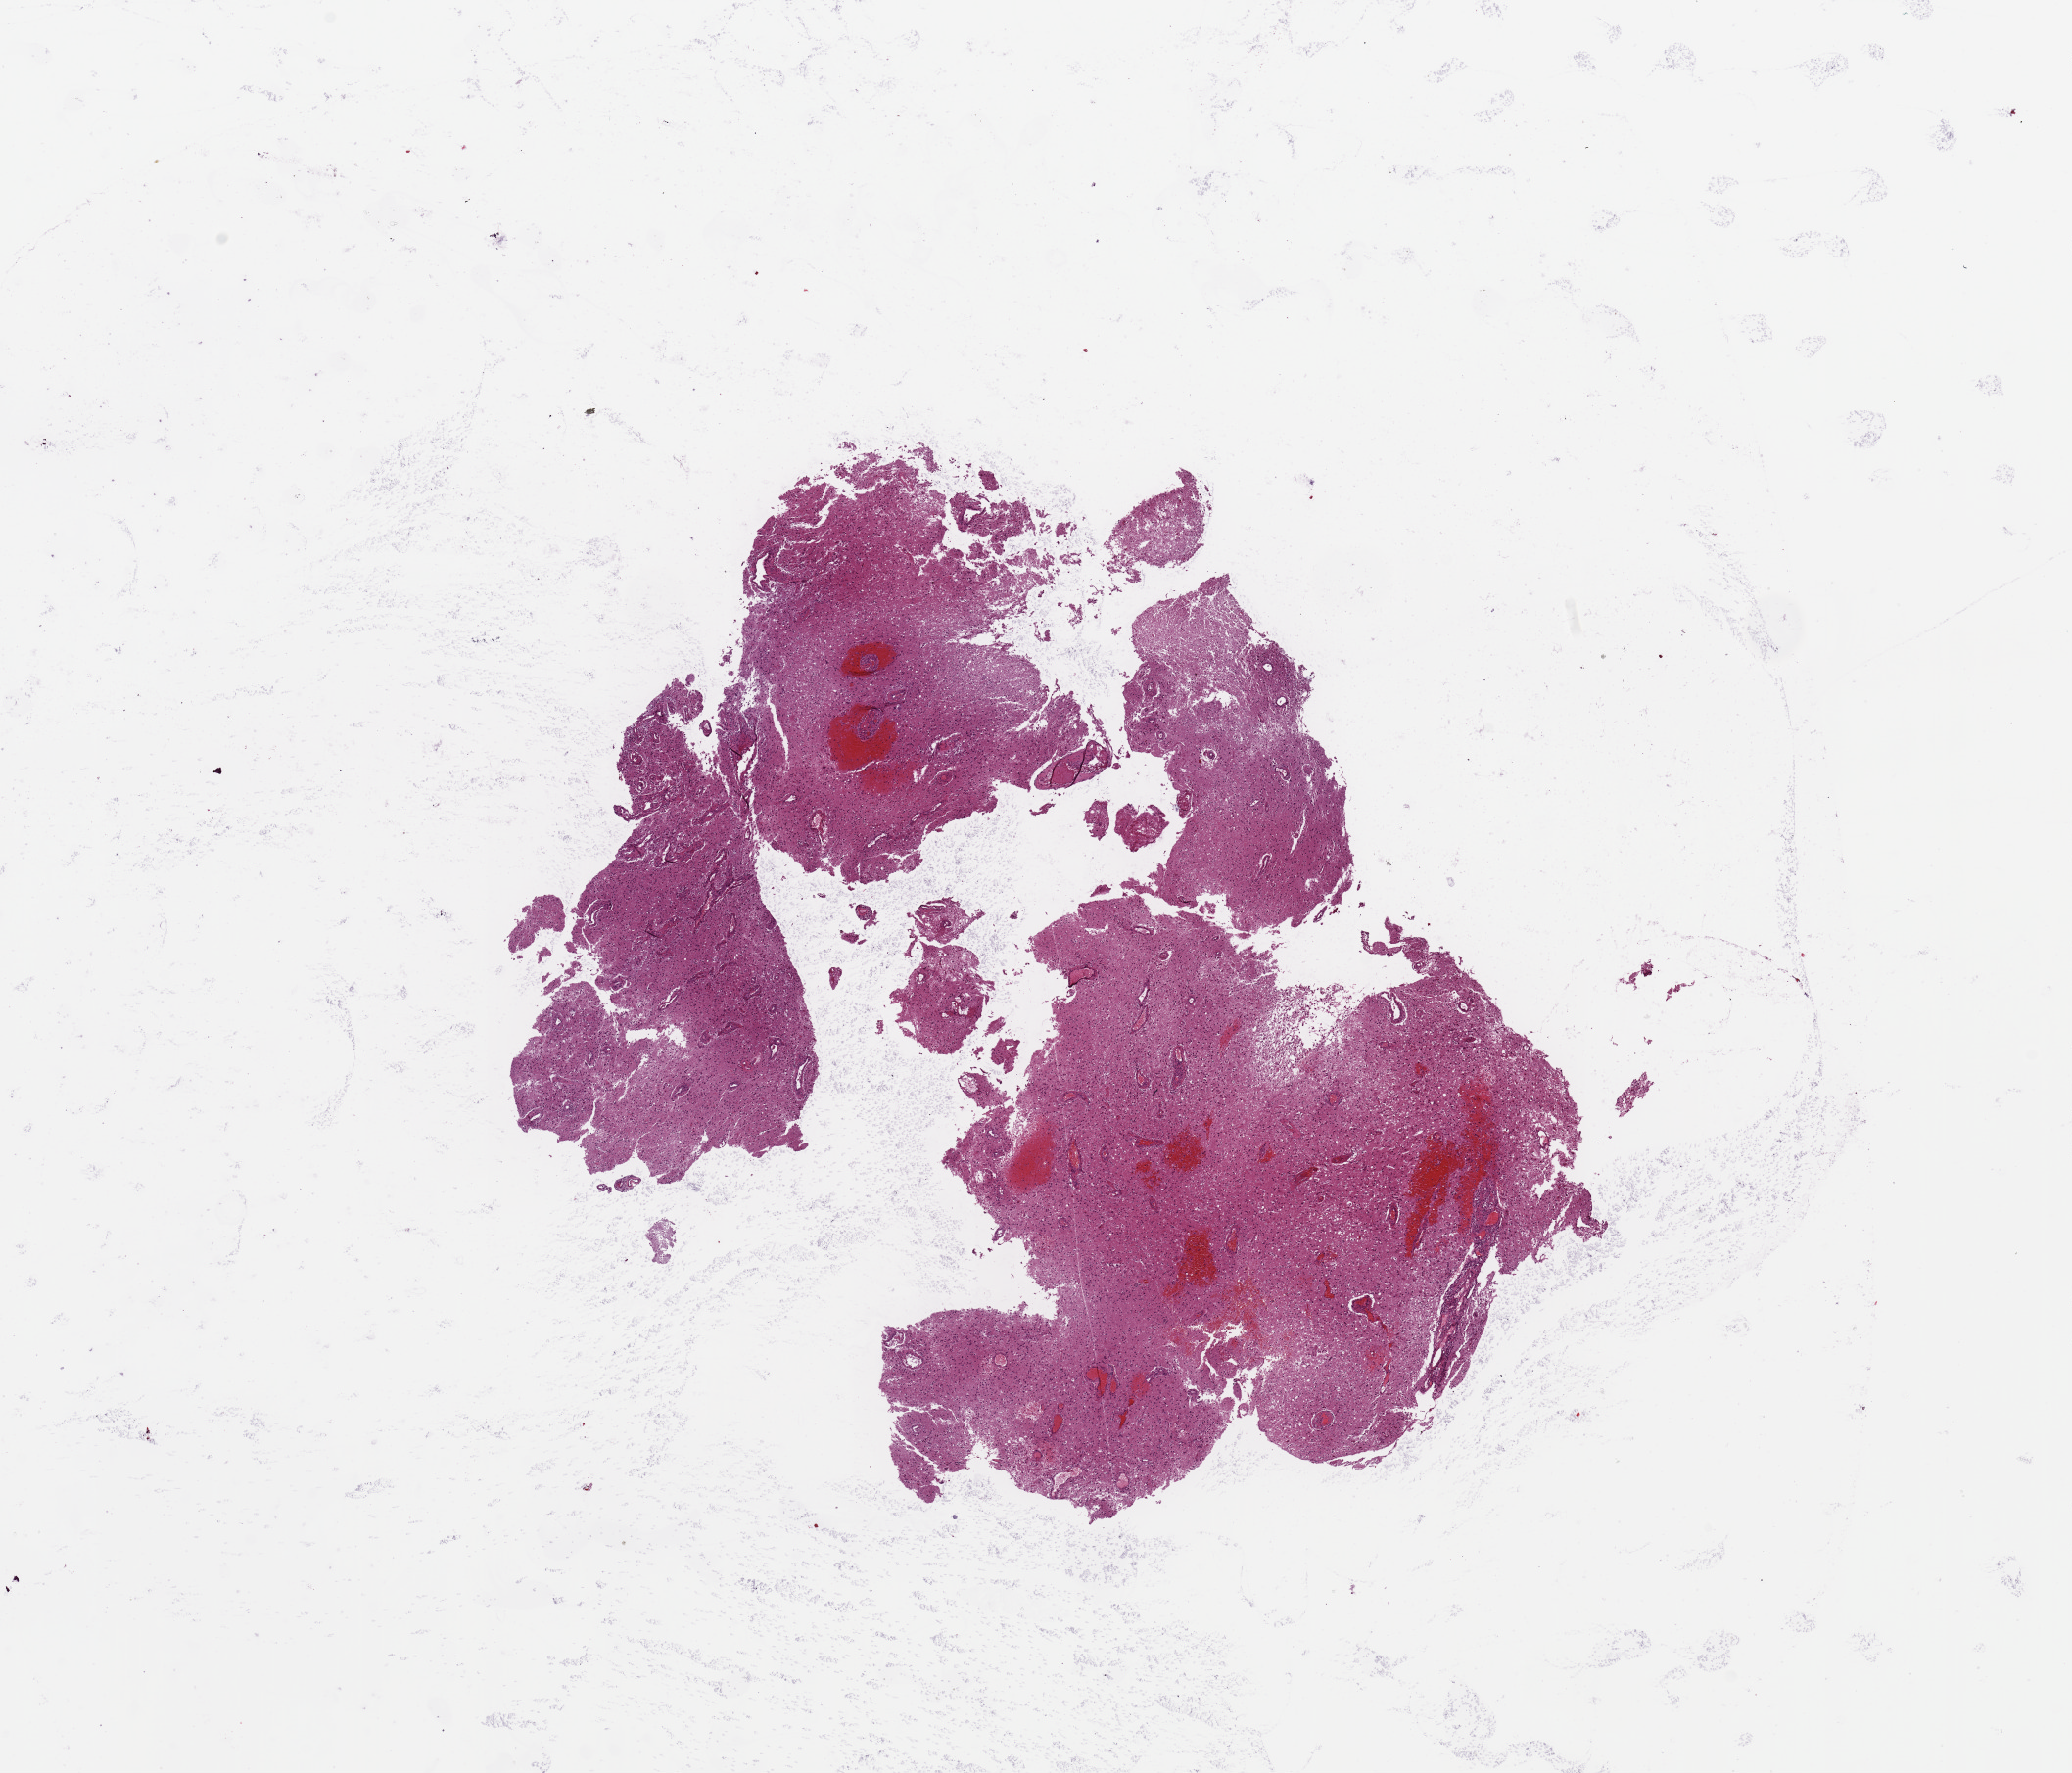
H&E whole-slide image — whole scanned area (about 16.7 x 14.3 mm) shown as a low-resolution overview. Tumour tissue sample, sampled site: brain. 53-year-old male patient. Slide review estimates, as recorded: tumour nuclei 70%, necrosis 5%.
Diagnosis: Glioblastoma.